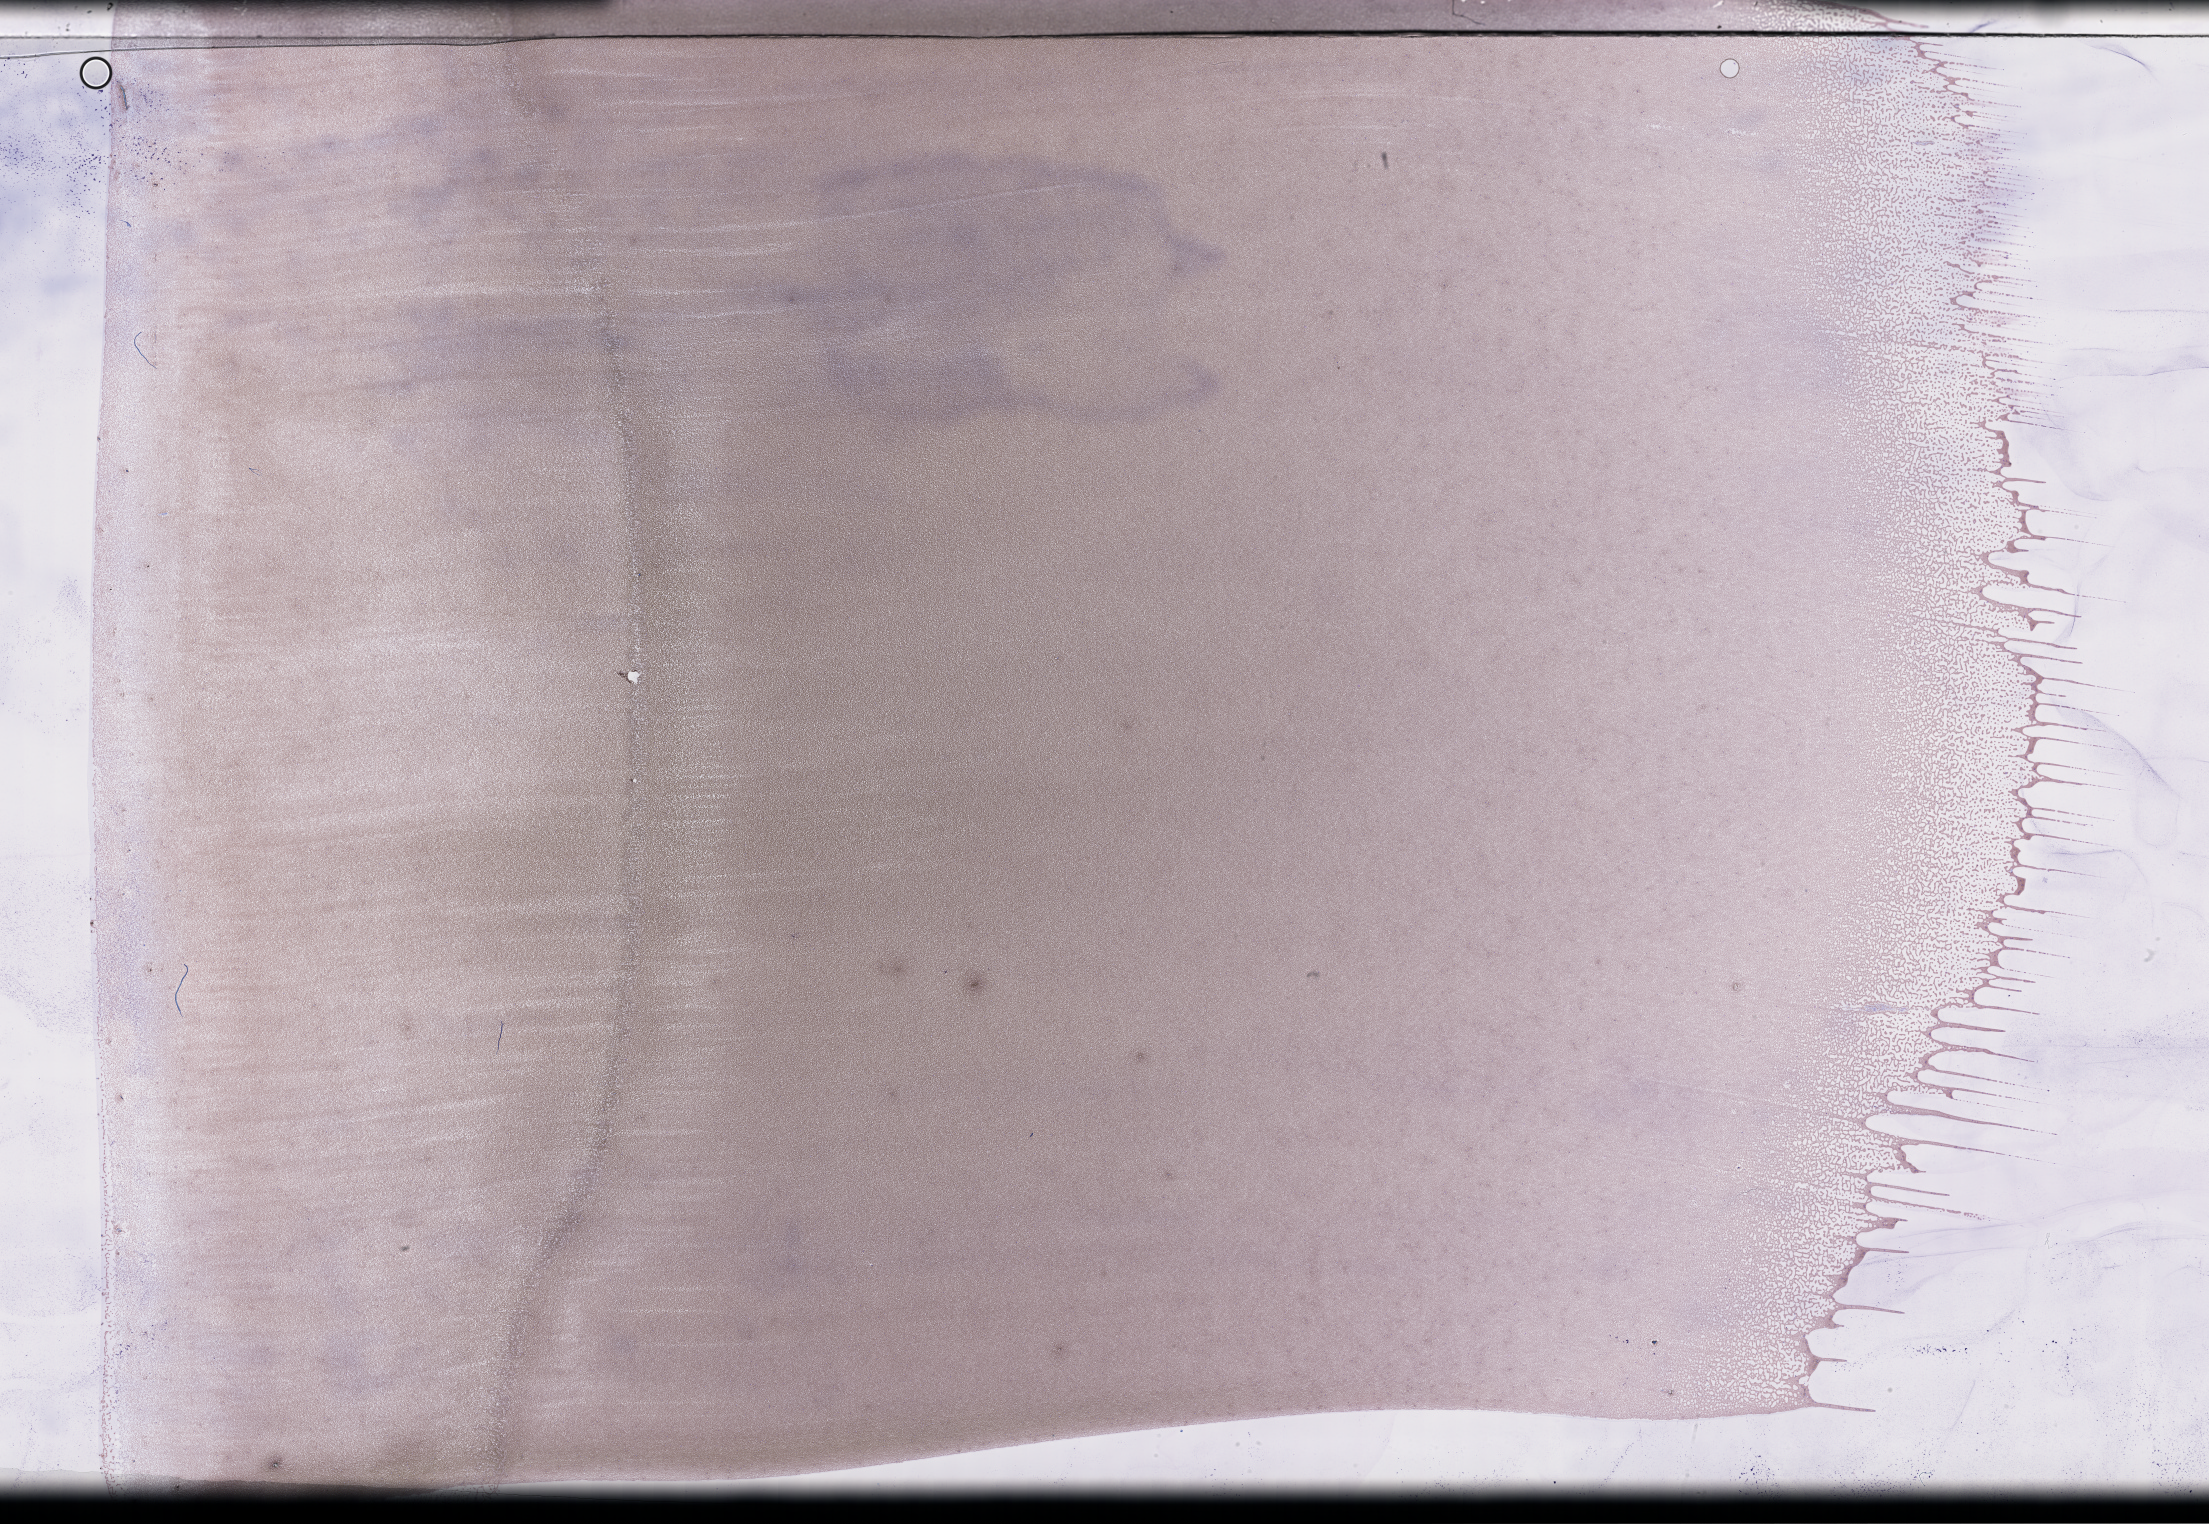
Whole-slide image of a whole blood smear, Wright-Giemsa stain — shown as a low-resolution overview of the whole scanned area (about 35.7 x 24.6 mm). Smear from an EDTA sample. Specimen time point: collected on treatment. Patient: female.
- from a patient with: Plasma Cell Myeloma